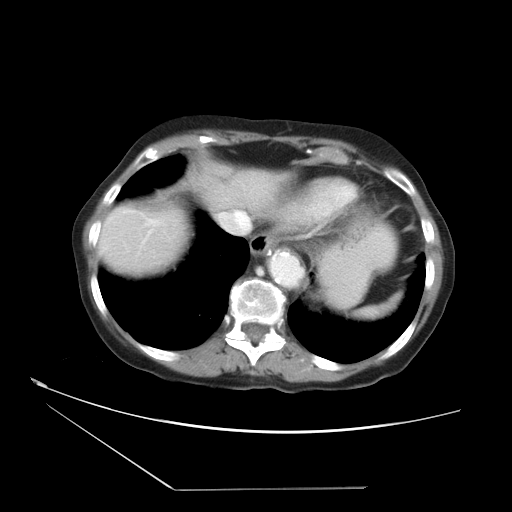
Contrast-enhanced abdominal CT, one axial slice. Position 31 of 36 along the scan axis. 120 kVp. Intravenous contrast given. Soft-tissue window (W 400 / L 40 HU). 5 mm slice thickness. 512 × 512 image matrix. Female patient, age 81 years. From the clinical record (not read from this slice): diagnosis: colorectal cancer liver metastases, imaged before liver resection; multiple liver metastases: no; largest metastasis: 1.6 cm; disease in both lobes: no.
Outlined on this slice (expert manual segmentation):
- hepatic veins: box from (x=219, y=211) to (x=245, y=217) px
- liver: (x=99, y=199)–(x=190, y=275)
- planned liver remnant (the part of the liver to remain after resection): (x=99, y=199)–(x=190, y=275)